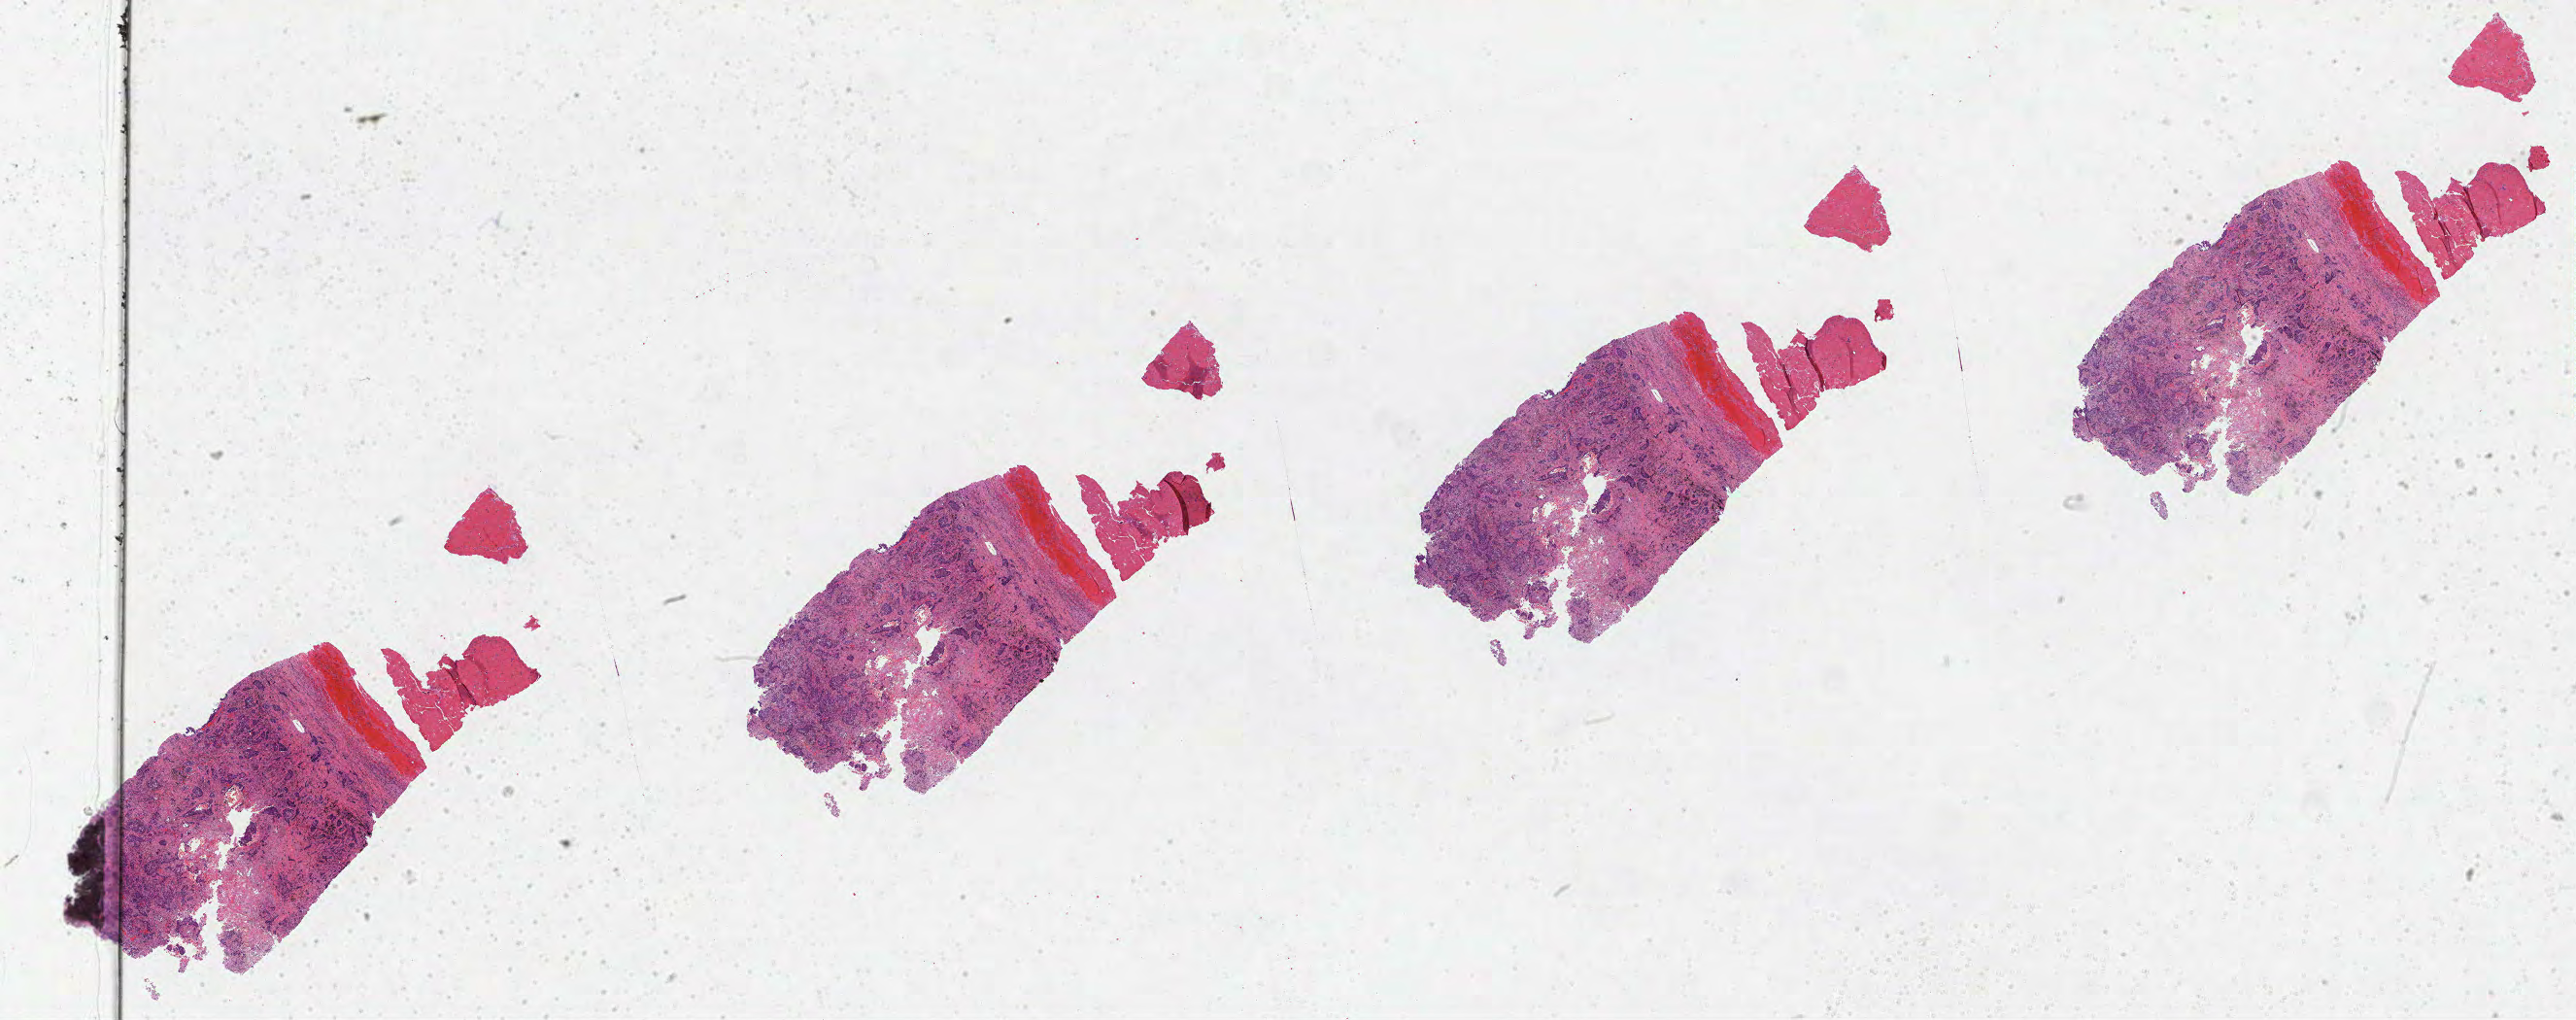
Whole-slide histology image, Hematoxylin and eosin (H&E) stained, whole scanned area (about 42.8 x 16.9 mm, from a 40x scan) shown as a low-resolution overview. Formalin-fixed paraffin-embedded (FFPE) diagnostic section. Lung, primary tumour sample. Male patient; age at initial diagnosis 70 years.
Histologic diagnosis: Squamous cell carcinoma, NOS (upper lobe, lung).